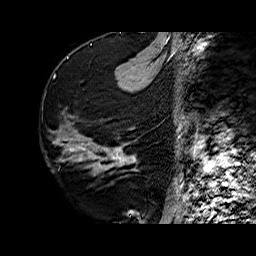
Breast MRI (dynamic contrast-enhanced), one sagittal slice; position 23 of 60 along the scan axis; dynamic contrast-enhanced series, time point 2 of 6 at this slice position (early post-contrast); 1.5 T; TE 6.4 ms, TR 32.7 ms; 256 × 256 image matrix, field of view 200 × 200 mm. Female patient. From the clinical record (not read from this slice): setting: breast cancer imaged before/during neoadjuvant chemotherapy; receptor status: HR-positive, HER2-negative.
Annotated regions visible in this slice (semi-automatically segmented with operator editing):
- analysis volume of interest (the breast-tissue region the enhancement analysis was run in; not a lesion): box from (x=73, y=116) to (x=138, y=176) px
- tumour enhancement mask (voxels above the 100 % enhancement threshold inside the analysis volume of interest): (x=112, y=148)–(x=135, y=164)